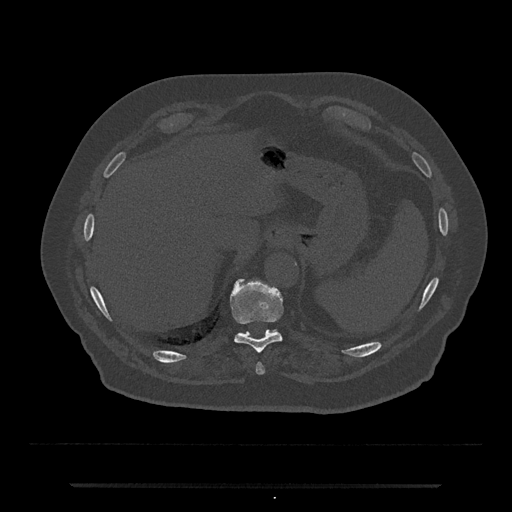
CT including the spine, one axial slice; reconstruction kernel Br40s/3; 120 kVp; bone window (W 1800 / L 400 HU); 0.5 mm slice thickness; 512 × 512 image matrix, field of view 434 × 434 mm. Patient: male, 80 years. Case-level facts recorded for this patient, not image findings: primary cancer: prostate; vertebrae with lytic lesions (as recorded): L1, T11.
Outlined on this slice (semi-automatically segmented with operator editing):
- T10 vertebra: bounding box [x1, y1, x2, y2] px = [229, 278, 283, 353]
- T11 vertebra: [271, 329, 278, 332]
- T9 vertebra: [256, 363, 265, 375]